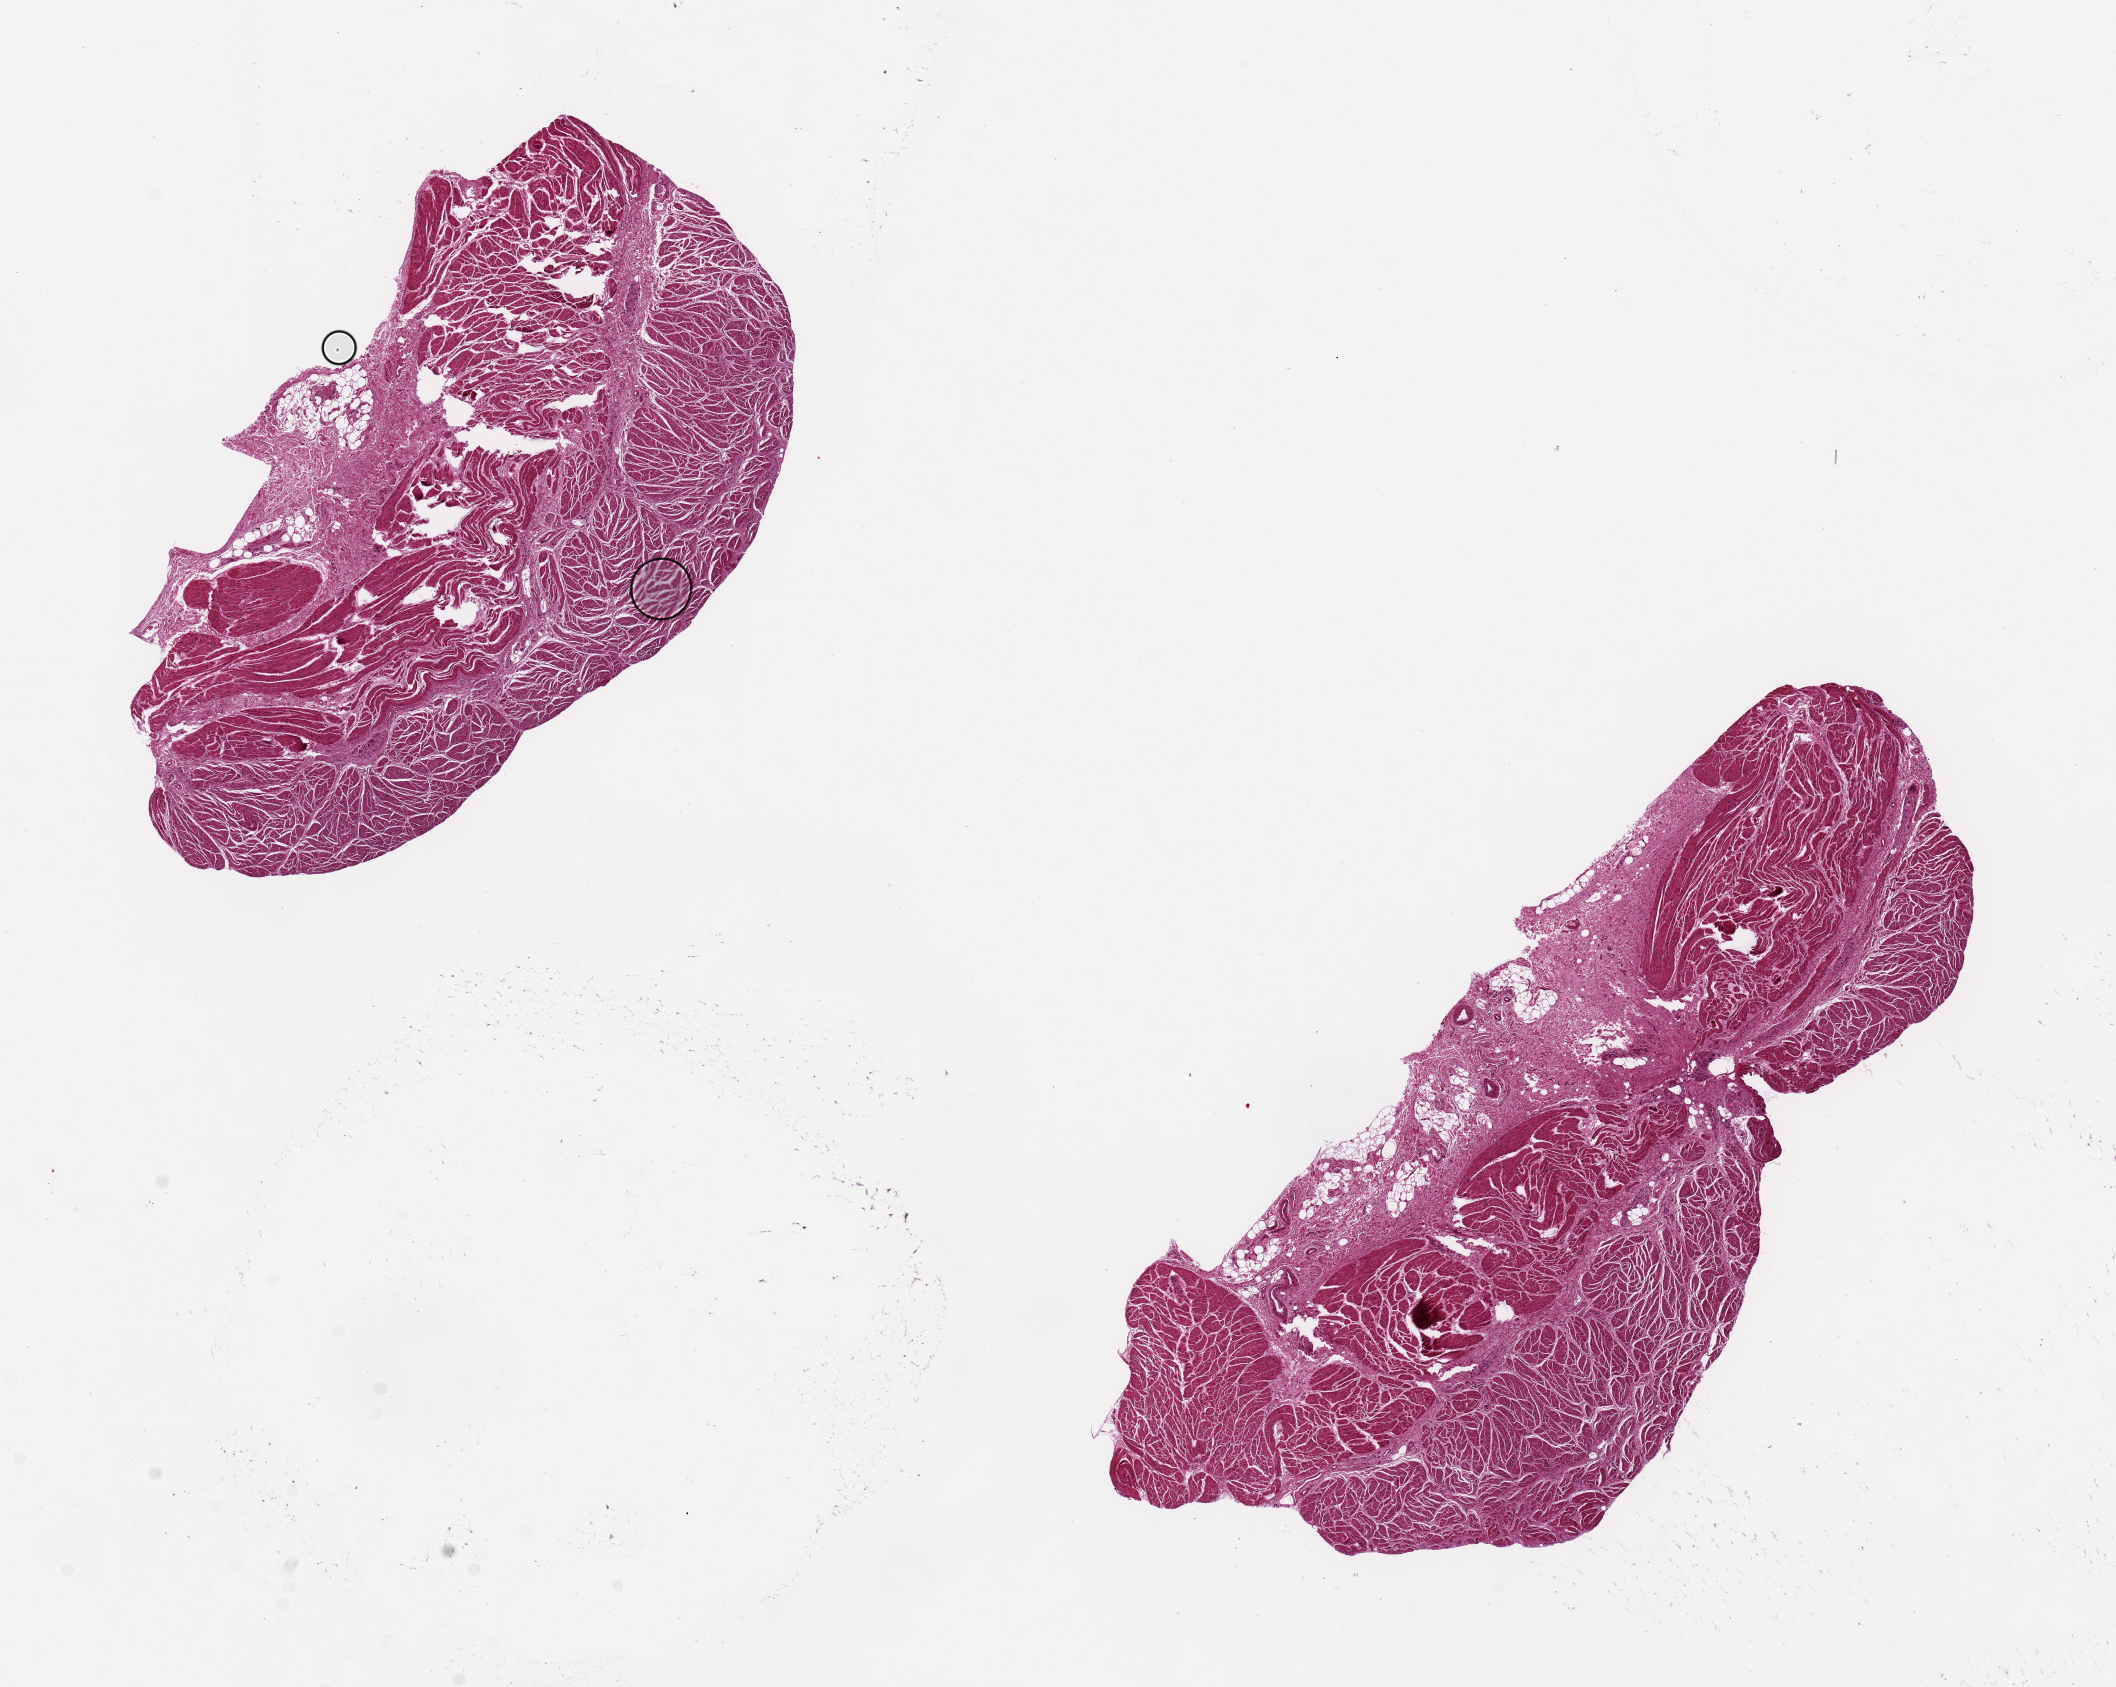
Digitized hematoxylin and eosin (H&E)-stained section — low-resolution overview of the scanned area, about 16.7 x 13.3 mm. PAXgene-fixed paraffin-embedded (PFPE) section. Section of esophageal muscle (target tissue). Tissue donor sample. Donor sex: male.
Reviewer comment on this tissue sample: 2 pieces, 9x4 mm.